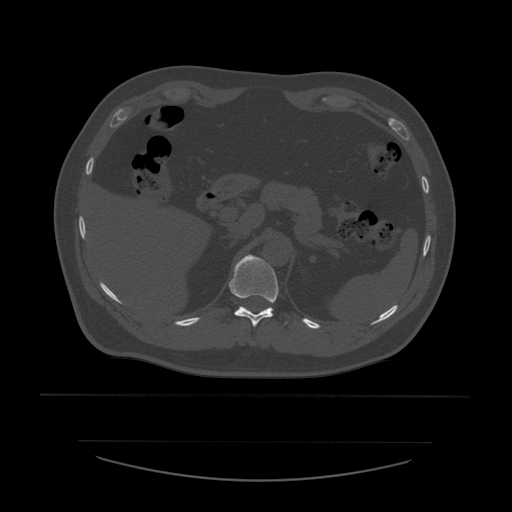
CT including the spine, one axial slice. Slice 273 of 532 in the series (ordered by position). Reconstruction kernel STANDARD. 120 kVp. Bone window (W 1800 / L 400 HU). 1.25 mm slice thickness. 512 × 512 image matrix. Patient age 44 years. Case-level facts recorded for this patient, not image findings: primary cancer: soft tissue sarcoma.
Structures marked on this image (semi-automatic segmentation, software-assisted and operator-edited):
- T11 vertebra: bounding box [x1, y1, x2, y2] px = [229, 255, 287, 327]